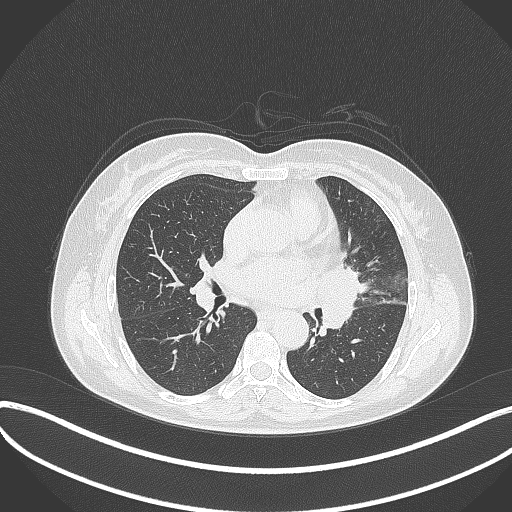
Chest CT, one axial slice; slice 183 of 373 in the series (ordered by position); reconstruction kernel B70f; 120 kVp; lung window (W 1500 / L -600 HU); 512 × 512 image matrix. Patient: female, 54 years. From the clinical record (not read from this slice): clinical TNM (as recorded): T2a N1 M0.
Structures marked on this image (bounding box drawn by a radiologist):
- lung tumour (recorded histology: small cell carcinoma): box from (x=315, y=260) to (x=364, y=340) px